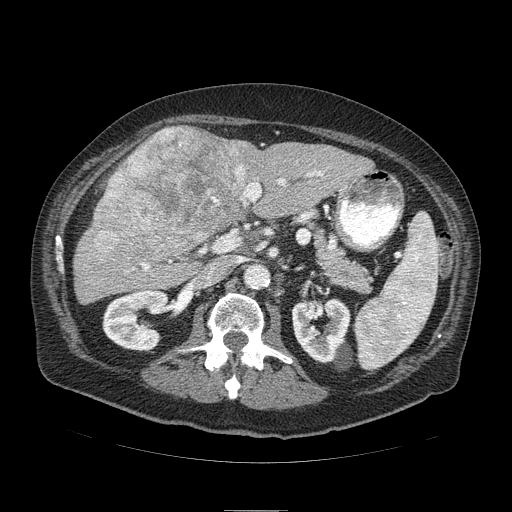
Contrast-enhanced abdominal CT (liver protocol), one axial slice; position 43 of 103 along the scan axis; reconstruction kernel STANDARD; soft-tissue window (W 400 / L 40 HU); 2.5 mm slice thickness; 512 × 512 image matrix. Case-level facts recorded for this patient, not image findings: diagnosis: hepatocellular carcinoma (patient treated with transarterial chemoembolisation; whether this scan precedes or follows treatment is not stated here); TNM stage (as recorded): Stage-IIIA; Child-Pugh class: B.
Annotated regions visible in this slice (semi-automatically segmented with operator editing):
- liver parenchyma outside the tumour (the mass and vessels are separate outlines, so this box may not span the whole liver): box from (x=74, y=136) to (x=374, y=302) px
- mass: (x=89, y=126)–(x=256, y=260)
- liver vessels: (x=133, y=171)–(x=322, y=271)